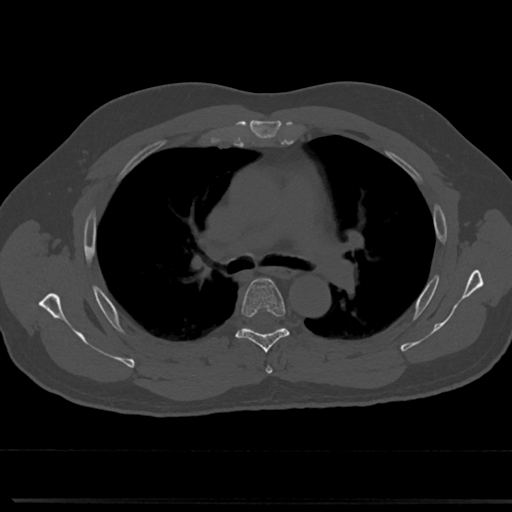
CT including the spine, one axial slice. Position 497 of 817 along the scan axis. Reconstruction kernel Br40s/3. Bone window (W 1800 / L 400 HU). 512 × 512 image matrix, field of view 355 × 355 mm. Male patient, age 61 years. Case-level facts recorded for this patient, not image findings: primary cancer: prostate.
Structures marked on this image (semi-automatically segmented with operator editing):
- T4 vertebra: box from (x=264, y=357) to (x=273, y=374) px
- T5 vertebra: (x=218, y=277)–(x=306, y=350)